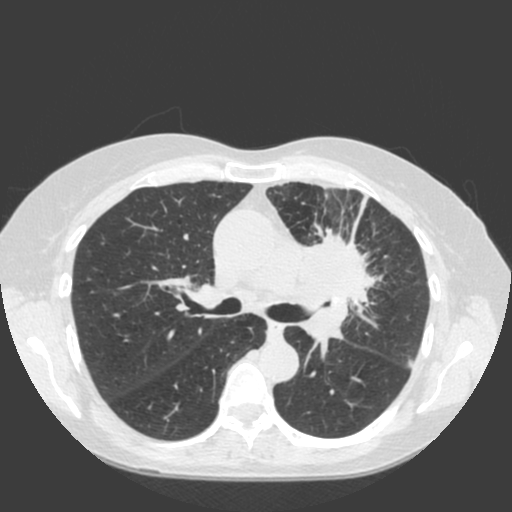
Axial slice from a low-dose chest CT screening exam; baseline screening round; lung window (W 1500 / L -600 HU); standard (soft-tissue) reconstruction kernel (C); 120 kVp; slice 66 of 184 in the series. Female participant, aged 66 years at enrolment. Current smoker at enrolment.
Expert reader's lesion annotation, box from (x=279, y=213) to (x=401, y=322) px. Screening reader's record for this exam (one nodule recorded; not confirmed to be the boxed lesion): non-calcified nodule or mass ≥4 mm, left upper lobe, 61 × 45 mm, spiculated (stellate) margins, soft tissue attenuation. Official screen result: positive, change unspecified: nodule(s) >= 4 mm or enlarging nodule(s), mass(es), or other non-specific abnormalities suspicious for lung cancer. Lung cancer was diagnosed 19 days after this screen: squamous cell carcinoma, keratinizing, NOS, left upper lobe, left hilum, mediastinum, left main stem bronchus, other location, poorly differentiated (G3), stage IIIB (AJCC 6th edition), 60 mm at pathology.